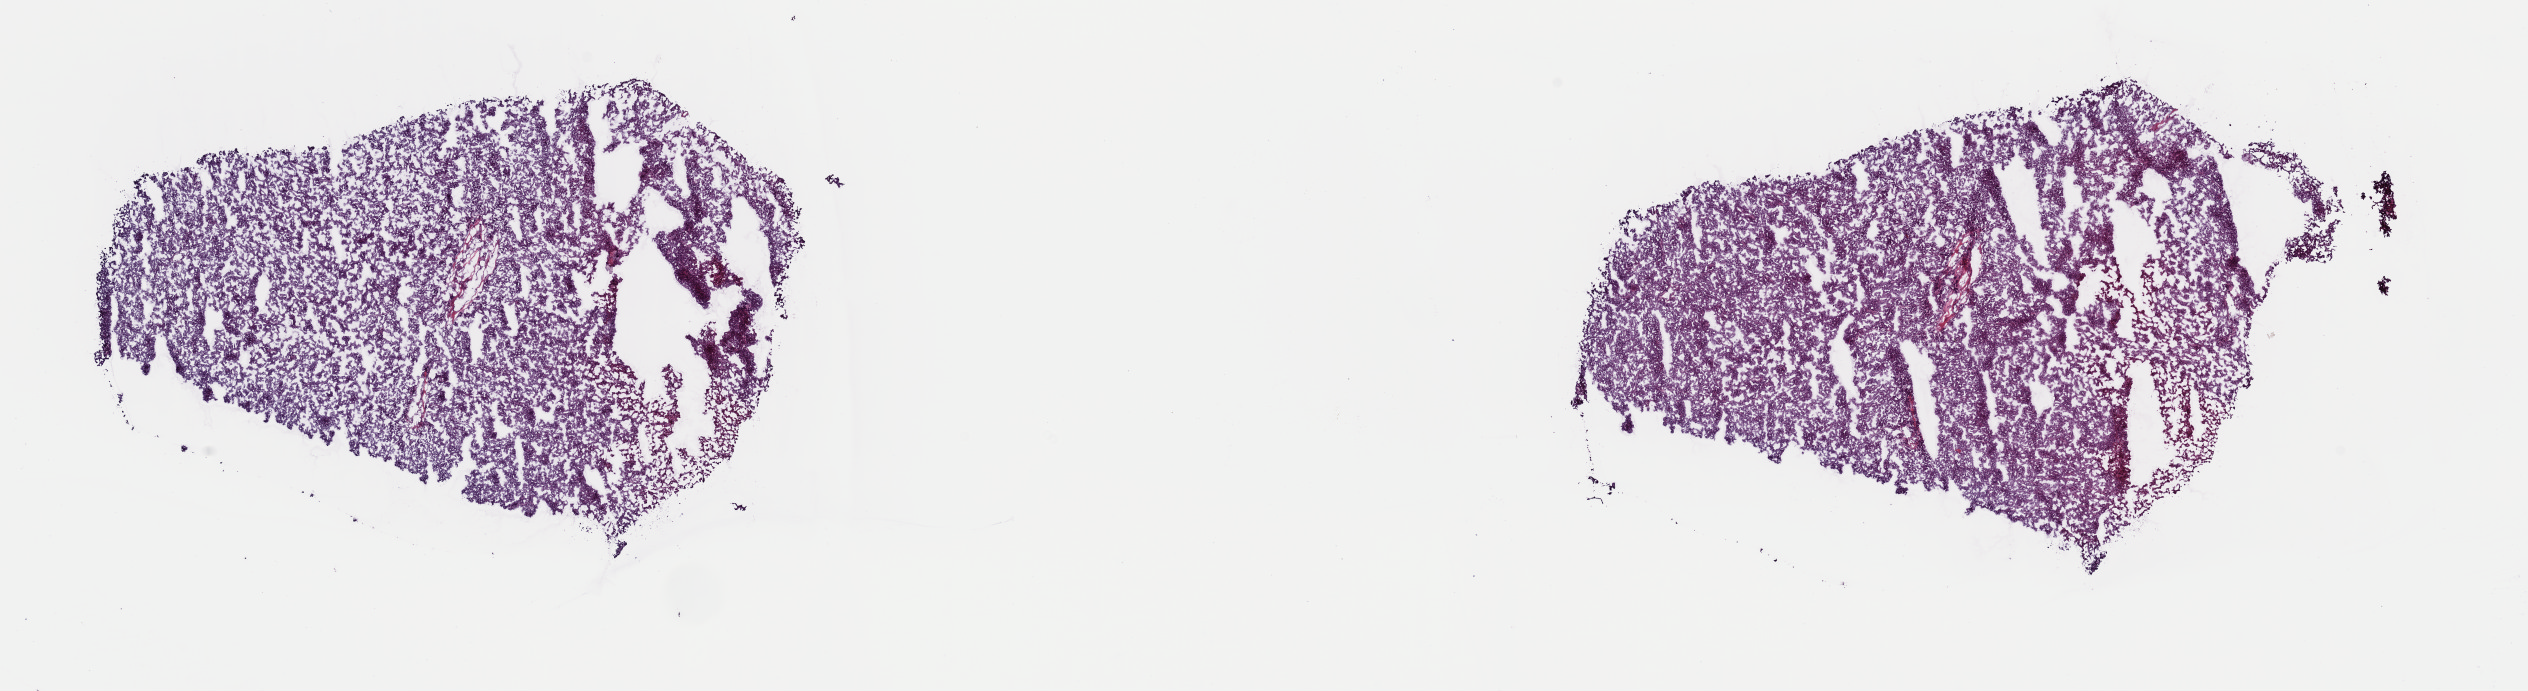
Hematoxylin and eosin (H&E) stained whole-slide image — low-resolution overview of the scanned area, about 20.0 x 5.5 mm (from a 40x scan), frozen section from the top of the tissue portion, adrenal cortex, primary tumour sample. Patient: female, age at initial diagnosis 17 years. Slide review estimates, as recorded: tumour cells 96%, tumour nuclei 100%, normal cells 0%, stromal cells 4%, necrosis 0%. Inflammatory infiltration, as recorded: lymphocyte infiltration 0%, monocyte infiltration 0%, neutrophil infiltration 0%.
- pathologic diagnosis: Adrenal cortical carcinoma (cortex of adrenal gland)
- laterality: left
- lymph nodes positive (case pathology): 1 of 1 examined